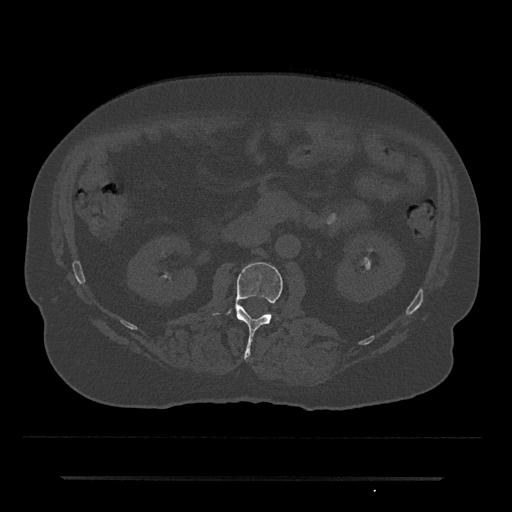
CT including the spine, one axial slice. Slice 6 of 797 in the series (ordered by position). Reconstruction kernel Br40s/3. 120 kVp. Bone window (W 1800 / L 400 HU). 0.5 mm slice thickness. 512 × 512 image matrix, field of view 437 × 437 mm. Male patient, age 69 years. Case-level facts recorded for this patient, not image findings: primary cancer: prostate.
Structures marked on this image (semi-automatic segmentation, software-assisted and operator-edited):
- L2 vertebra: bounding box (x1, y1, x2, y2) in pixels: (212, 262, 283, 359)